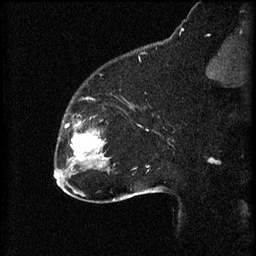
Breast MRI (dynamic contrast-enhanced), one sagittal slice; 3 images stored at this slice position (order not interpretable as contrast timing); 1.5 T; TE 4.2 ms, TR 8.2 ms; 2 mm slice thickness; 256 × 256 image matrix, field of view 180 × 180 mm. Patient: female, 32 years.
Annotated regions visible in this slice (semi-automatic segmentation, software-assisted and operator-edited):
- analysis volume of interest (the breast-tissue region the enhancement analysis was run in; not a lesion): bounding box (x1, y1, x2, y2) in pixels: (59, 114, 111, 165)
- tumour enhancement mask (voxels above the 70 % enhancement threshold inside the analysis volume of interest): (66, 122, 101, 161)